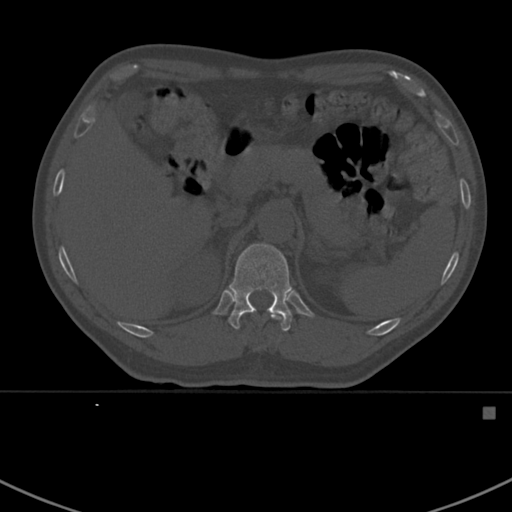
CT including the spine, one axial slice. Slice 334 of 412 in the series (ordered by position). 120 kVp. Bone window (W 1800 / L 400 HU). 1.5 mm slice thickness. 512 × 512 image matrix, field of view 358 × 358 mm. Patient: male, 59 years. From the clinical record (not read from this slice): primary cancer: prostate.
Annotated regions visible in this slice (semi-automatic segmentation, software-assisted and operator-edited):
- T11 vertebra: bounding box <271,314,282,320> (left, top, right, bottom; pixels)
- T12 vertebra: <228,243,293,331>